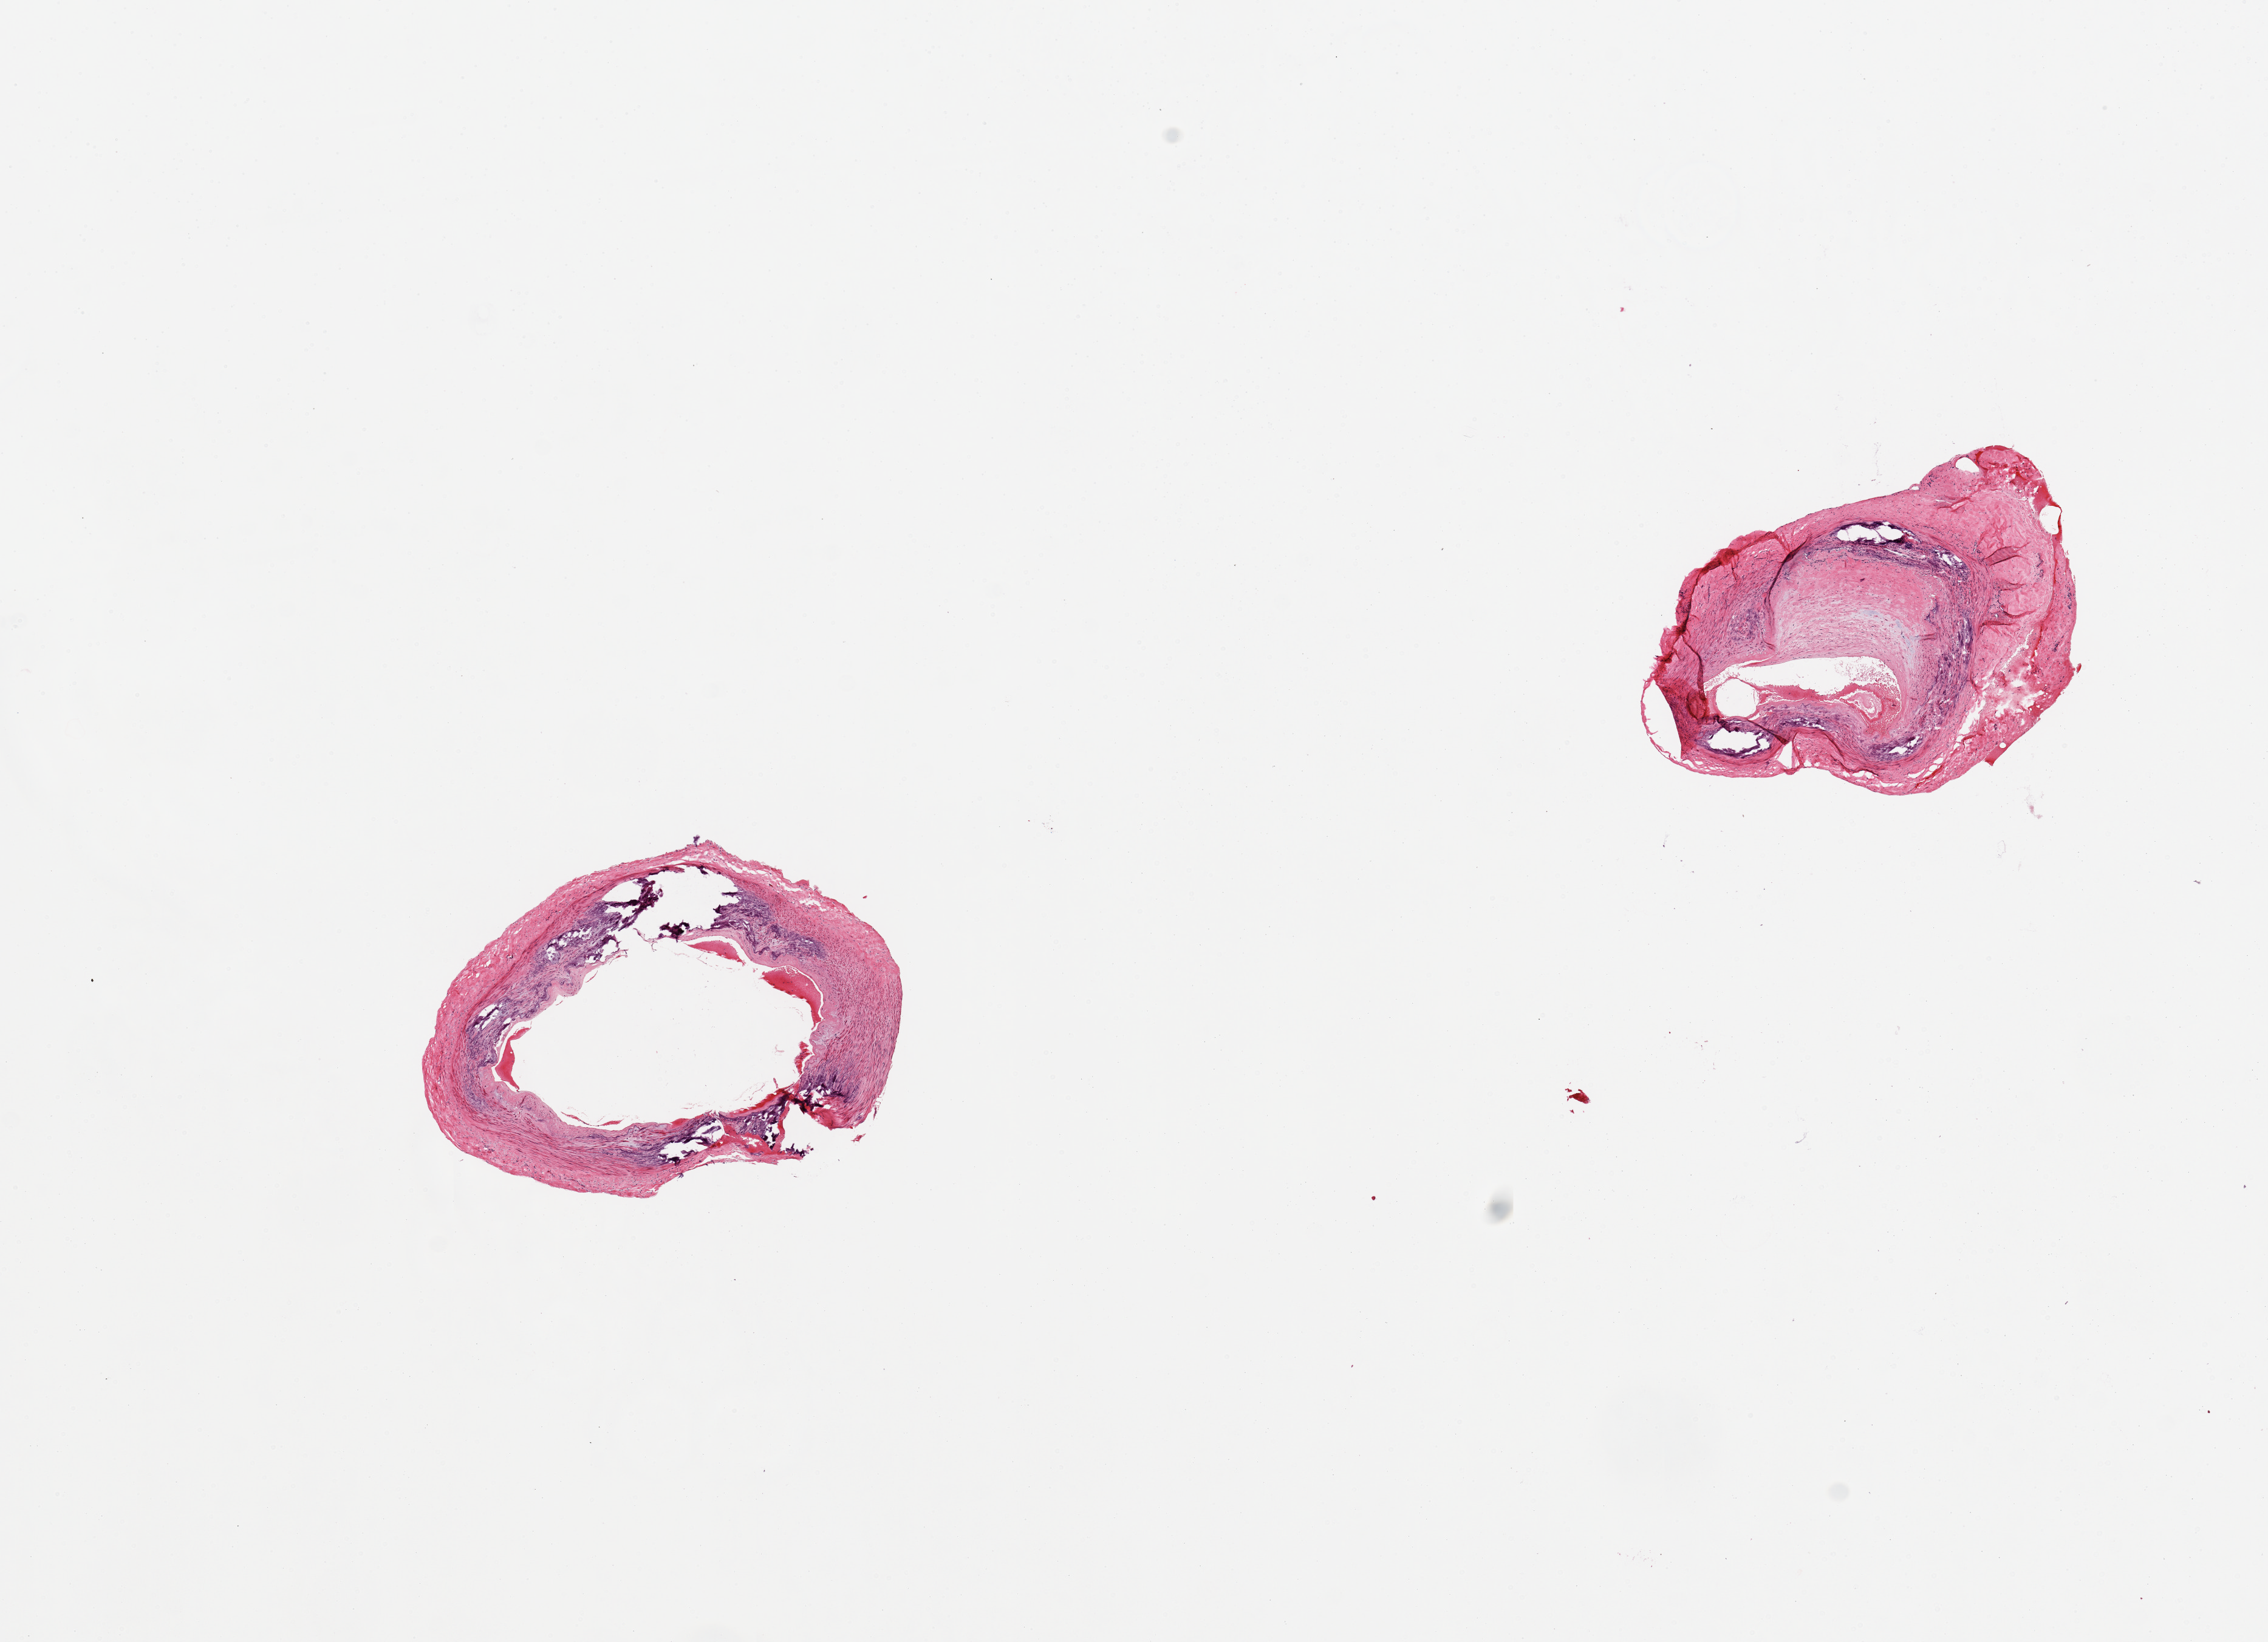
Whole-slide image, haematoxylin and eosin stain, brightfield, shown as a low-resolution overview of the whole scanned area (about 14.8 x 10.7 mm, from a 20x scan); PAXgene-fixed paraffin-embedded (PFPE) section; target tissue: tibial artery; donor tissue sample.
Review note (as recorded): 2 pieces; extensive calcified atheromatous plaque.